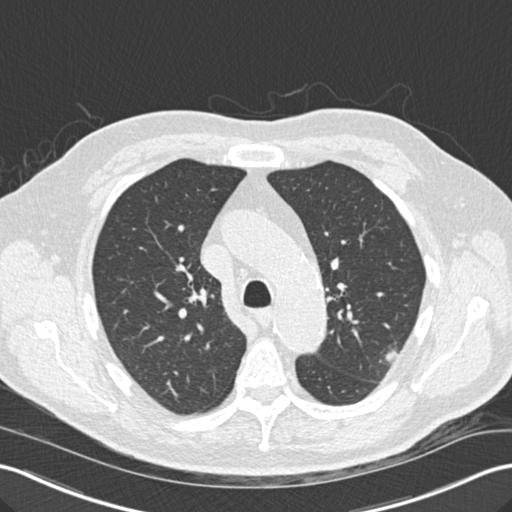
Low-dose screening chest CT, one axial slice; slice 108 of 157 in the series (ordered by position); reconstruction kernel B30f; 120 kVp; lung window (W 1500 / L -600 HU); 2 mm slice thickness; 512 × 512 image matrix.
Annotated regions visible in this slice (manually delineated by an expert):
- lesion 1 (tumor, upper lobe of left lung): box from (x=380, y=351) to (x=396, y=364) px